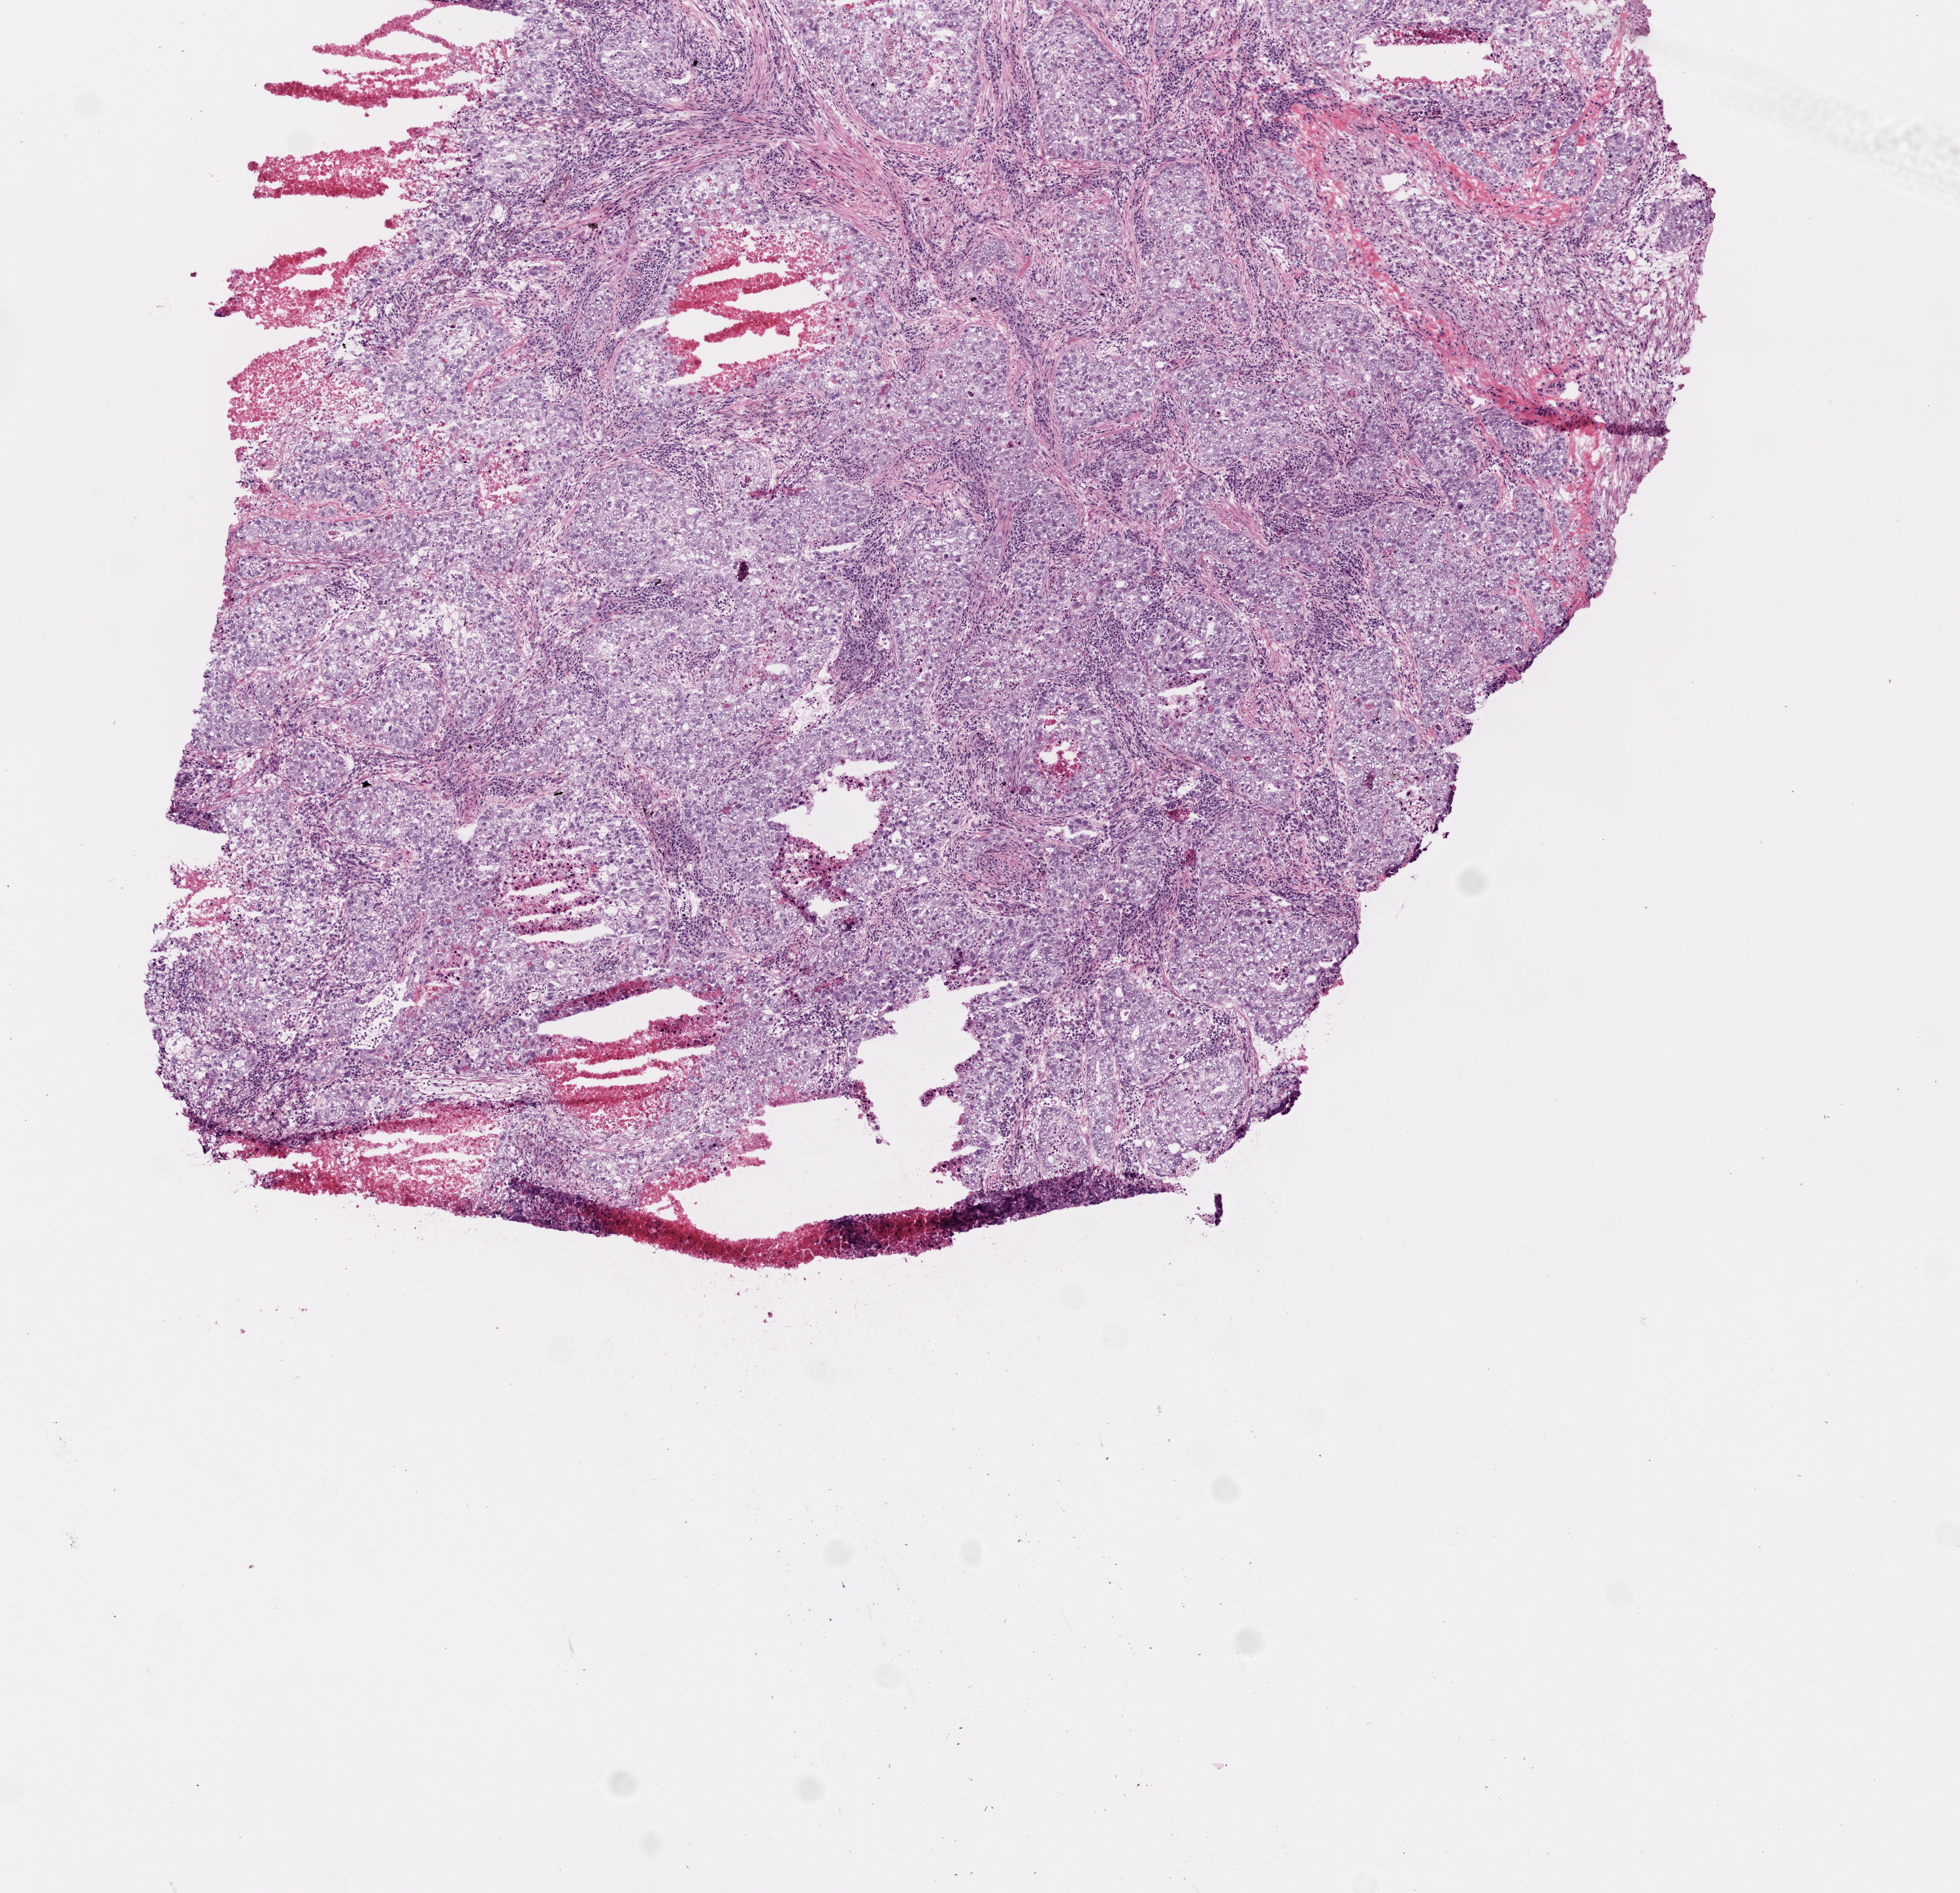
H&E whole-slide image, low-resolution overview of the scanned area, about 6.0 x 5.8 mm. Frozen section. Sample: primary tumour, lung. Patient: female, age at initial diagnosis 72 years. Slide review estimates, as recorded: tumour cells 85%, tumour nuclei 80%, normal cells 0%, stromal cells 5%, necrosis 10%.
AJCC pathologic stage: IB. Diagnosis: Adenocarcinoma, NOS (upper lobe, lung). TNM: T2 N0 M0. Laterality: left.